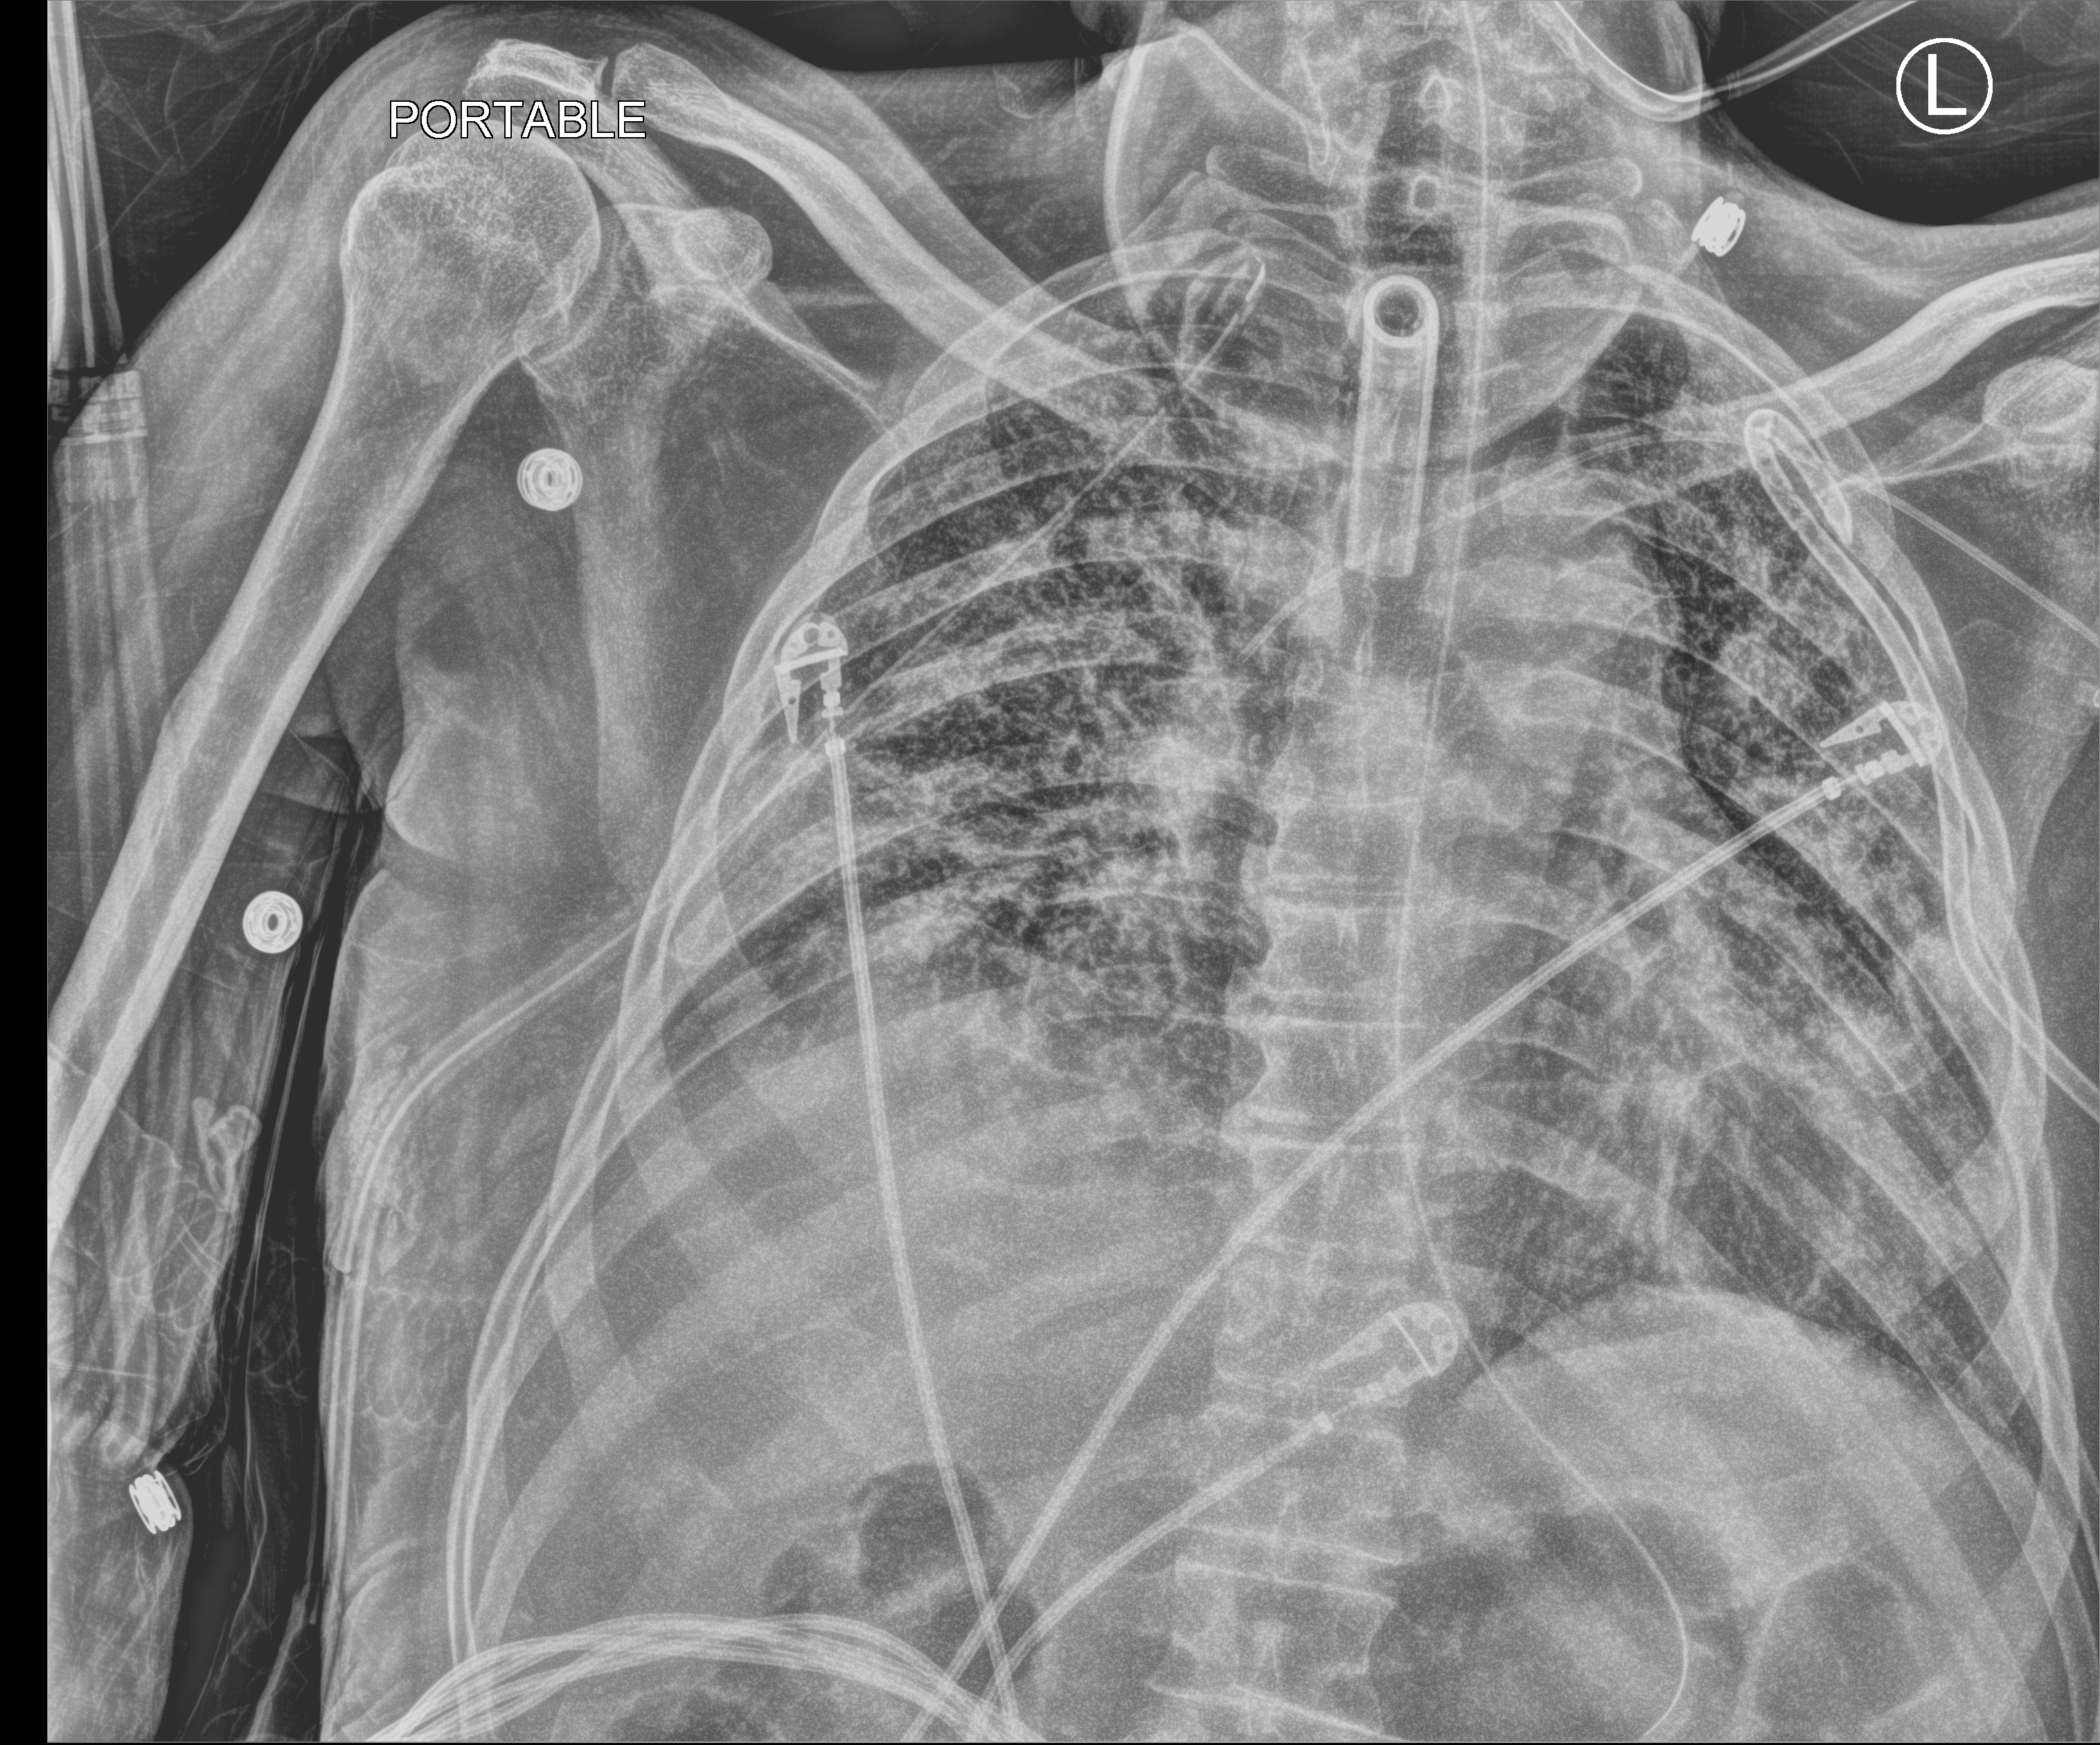
Chest X-ray (portable), anteroposterior (AP) projection. Male patient hospitalised with COVID-19, age 18–59 years.
Admission-level facts for this patient (not findings on this image; timing relative to this image not recorded): admitted to intensive care during this hospital stay: yes.